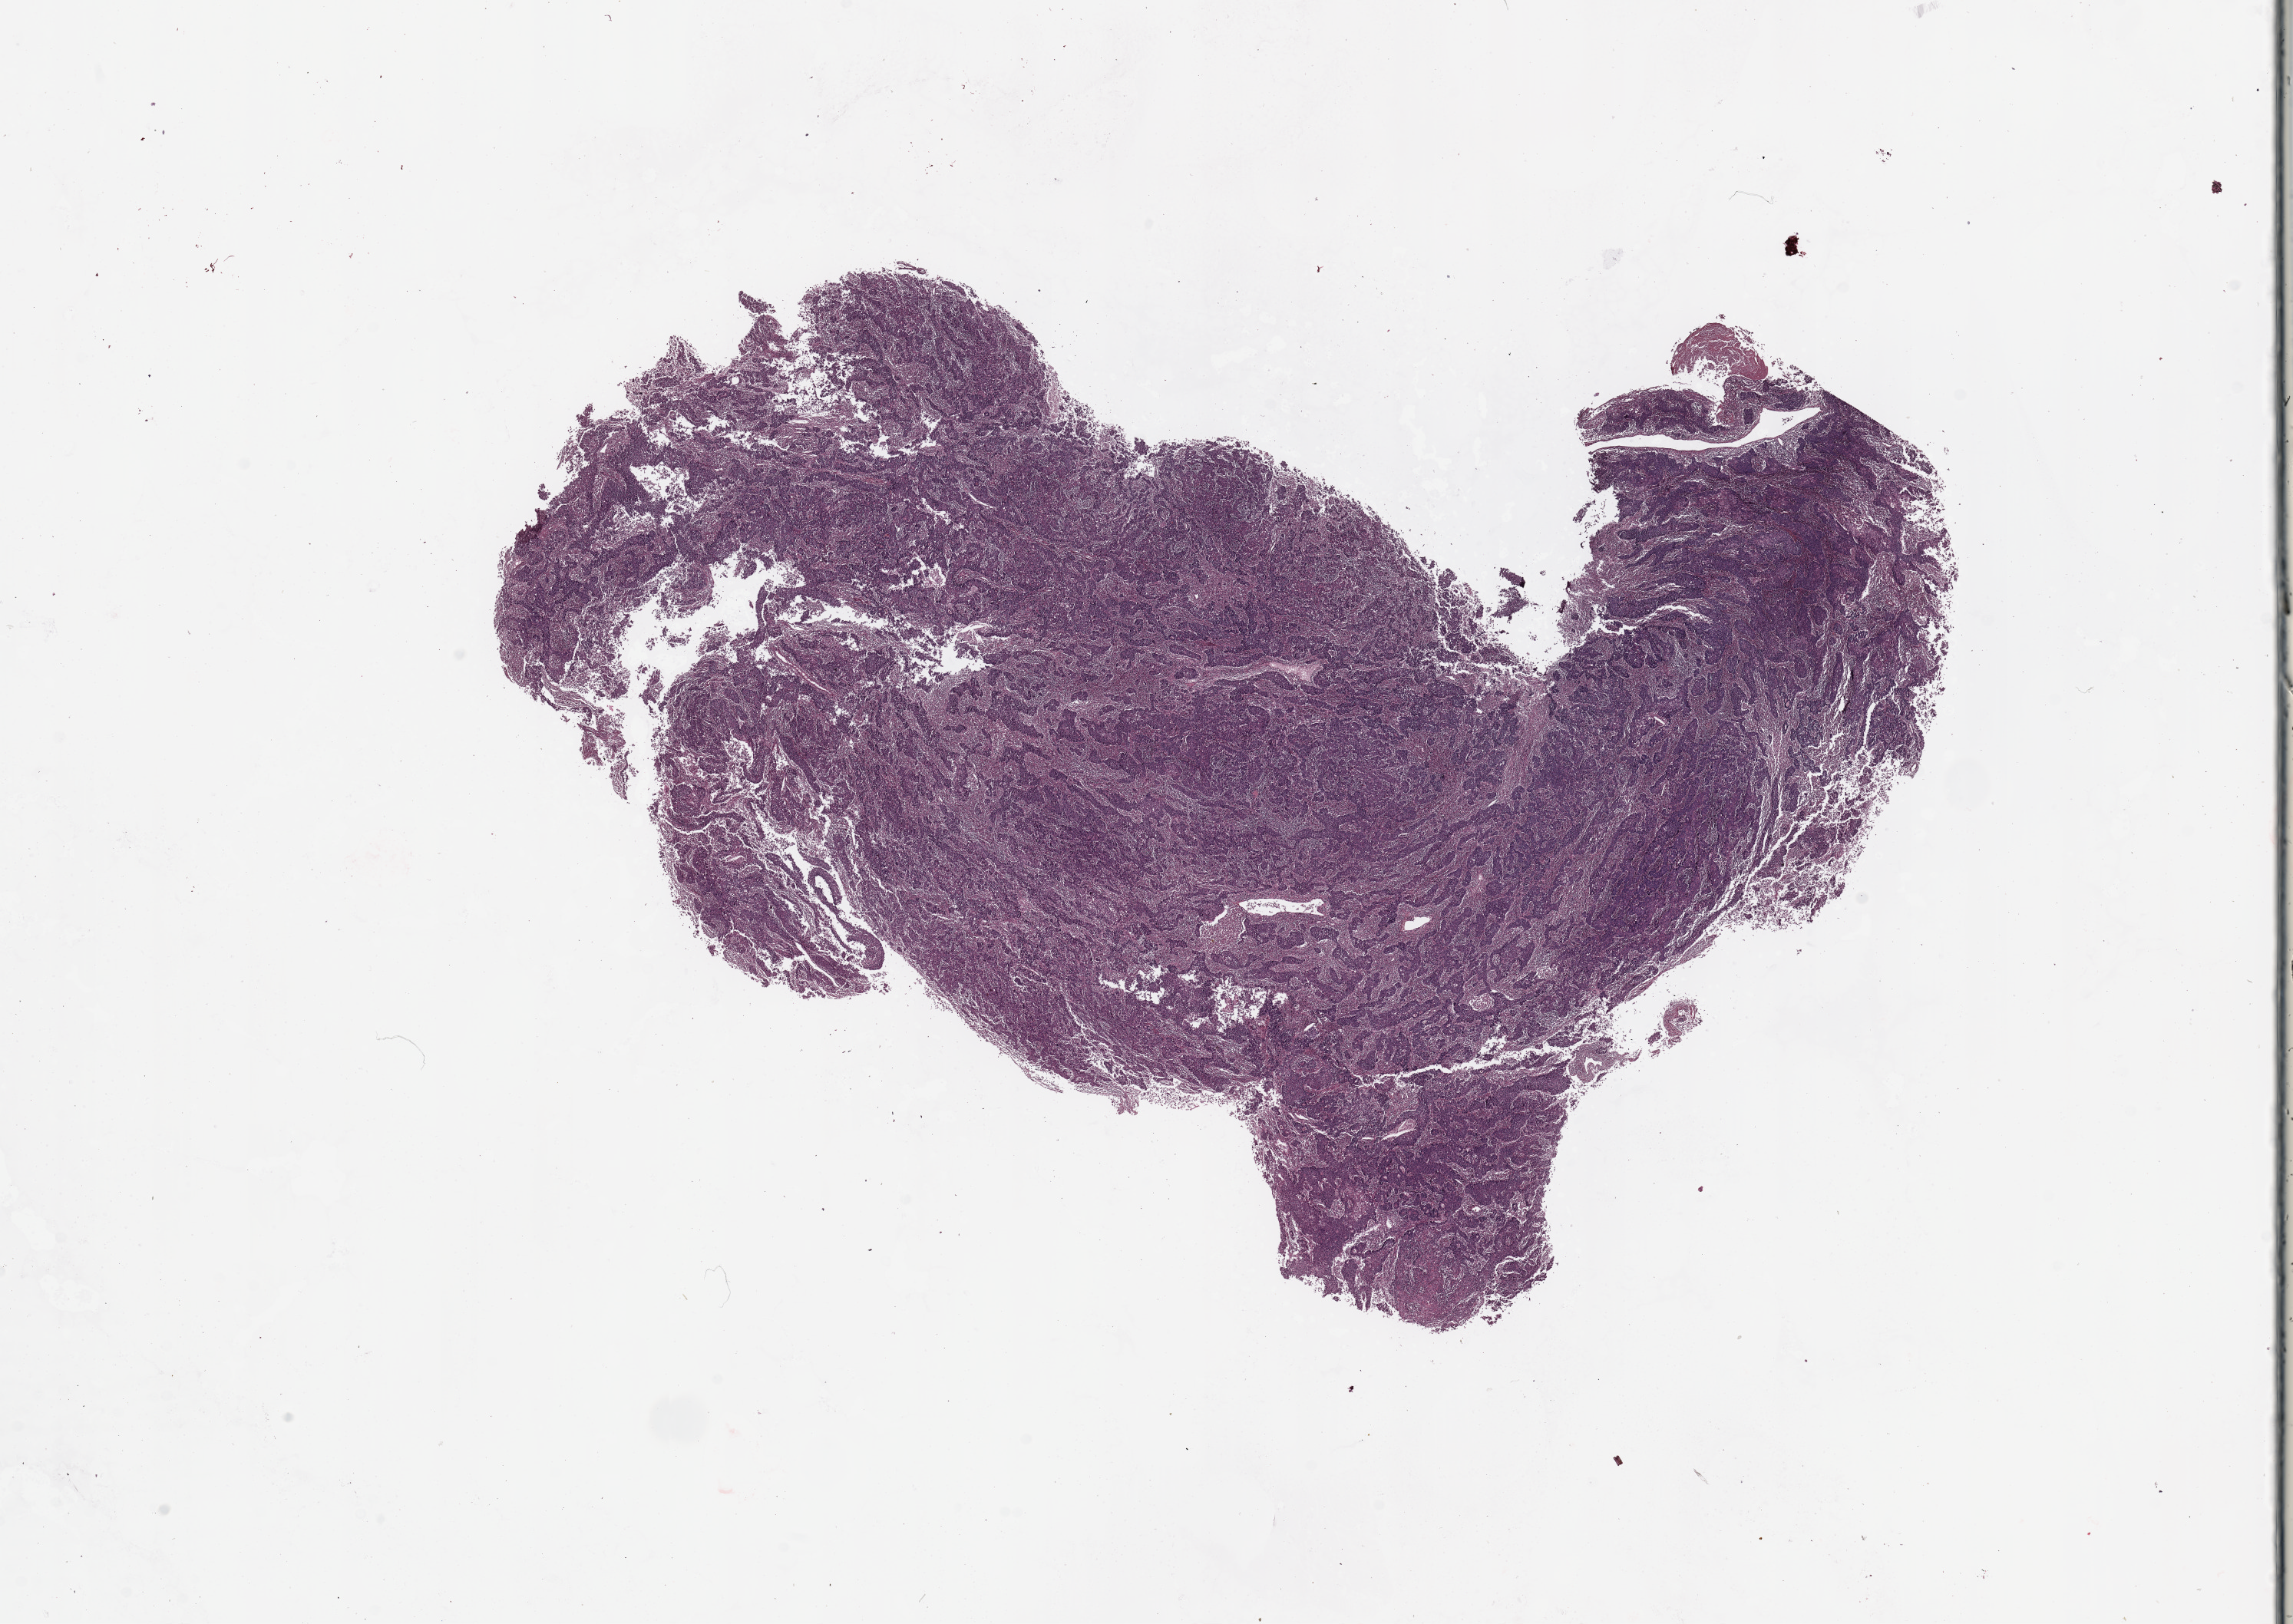
Whole-slide histology image, H&E-stained, shown as a low-resolution overview of the whole scanned area (about 23.6 x 16.7 mm, from a 20x scan); uterus, tumour tissue. Patient: female, age 58 years.
Histologic diagnosis: Endometrioid adenocarcinoma, NOS.